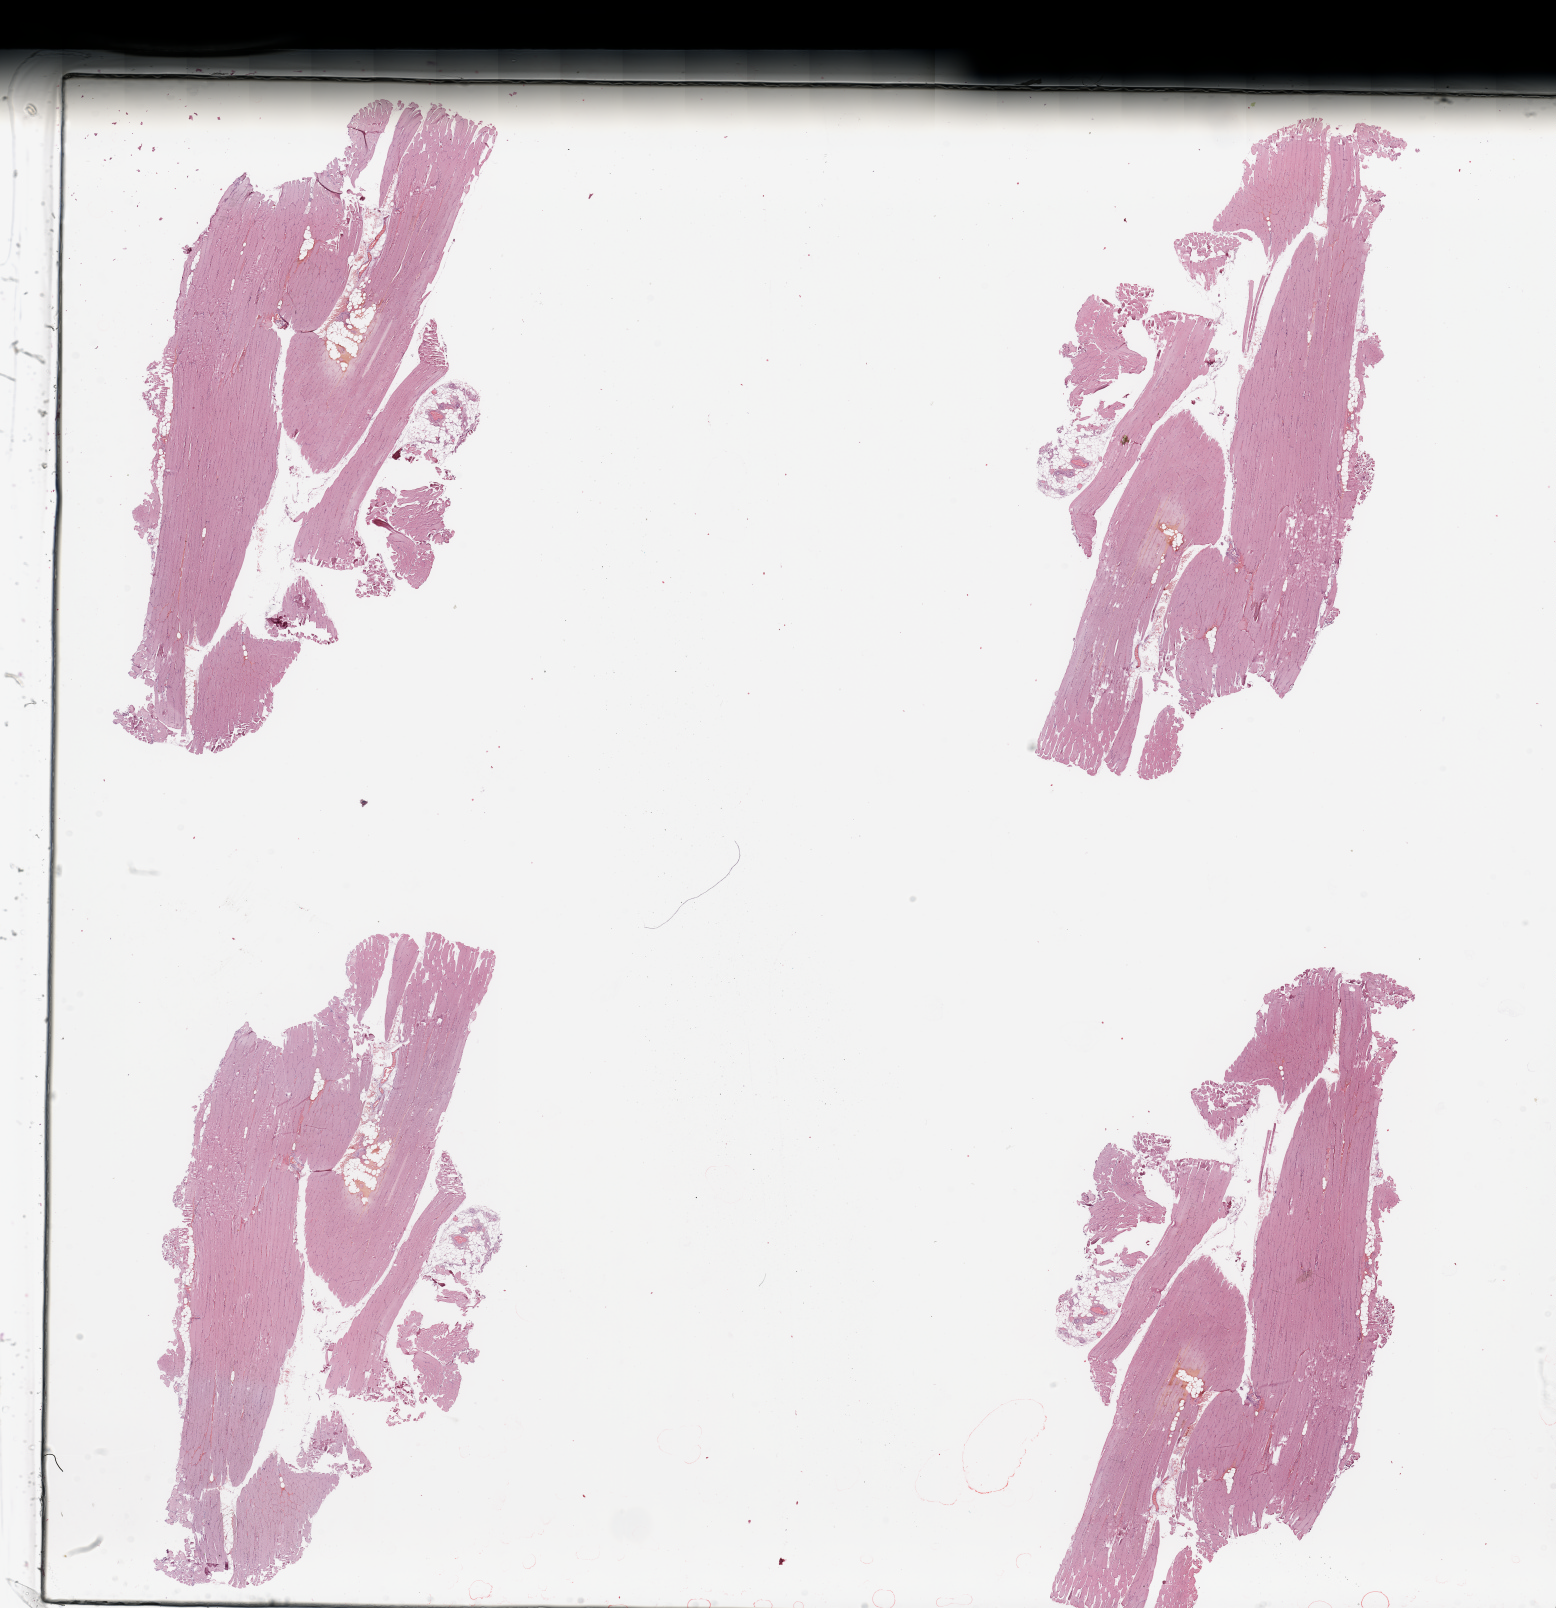
Whole-slide histology image, H&E, shown as a low-resolution overview of the whole scanned area (about 24.6 x 25.4 mm, from a 20x scan), normal (non-tumour) tissue sample. 70-year-old male patient.
This section: normal (non-tumour) tissue from the same patient. Patient diagnosis (cohort enrolment): sarcoma (site not recorded at cohort level).